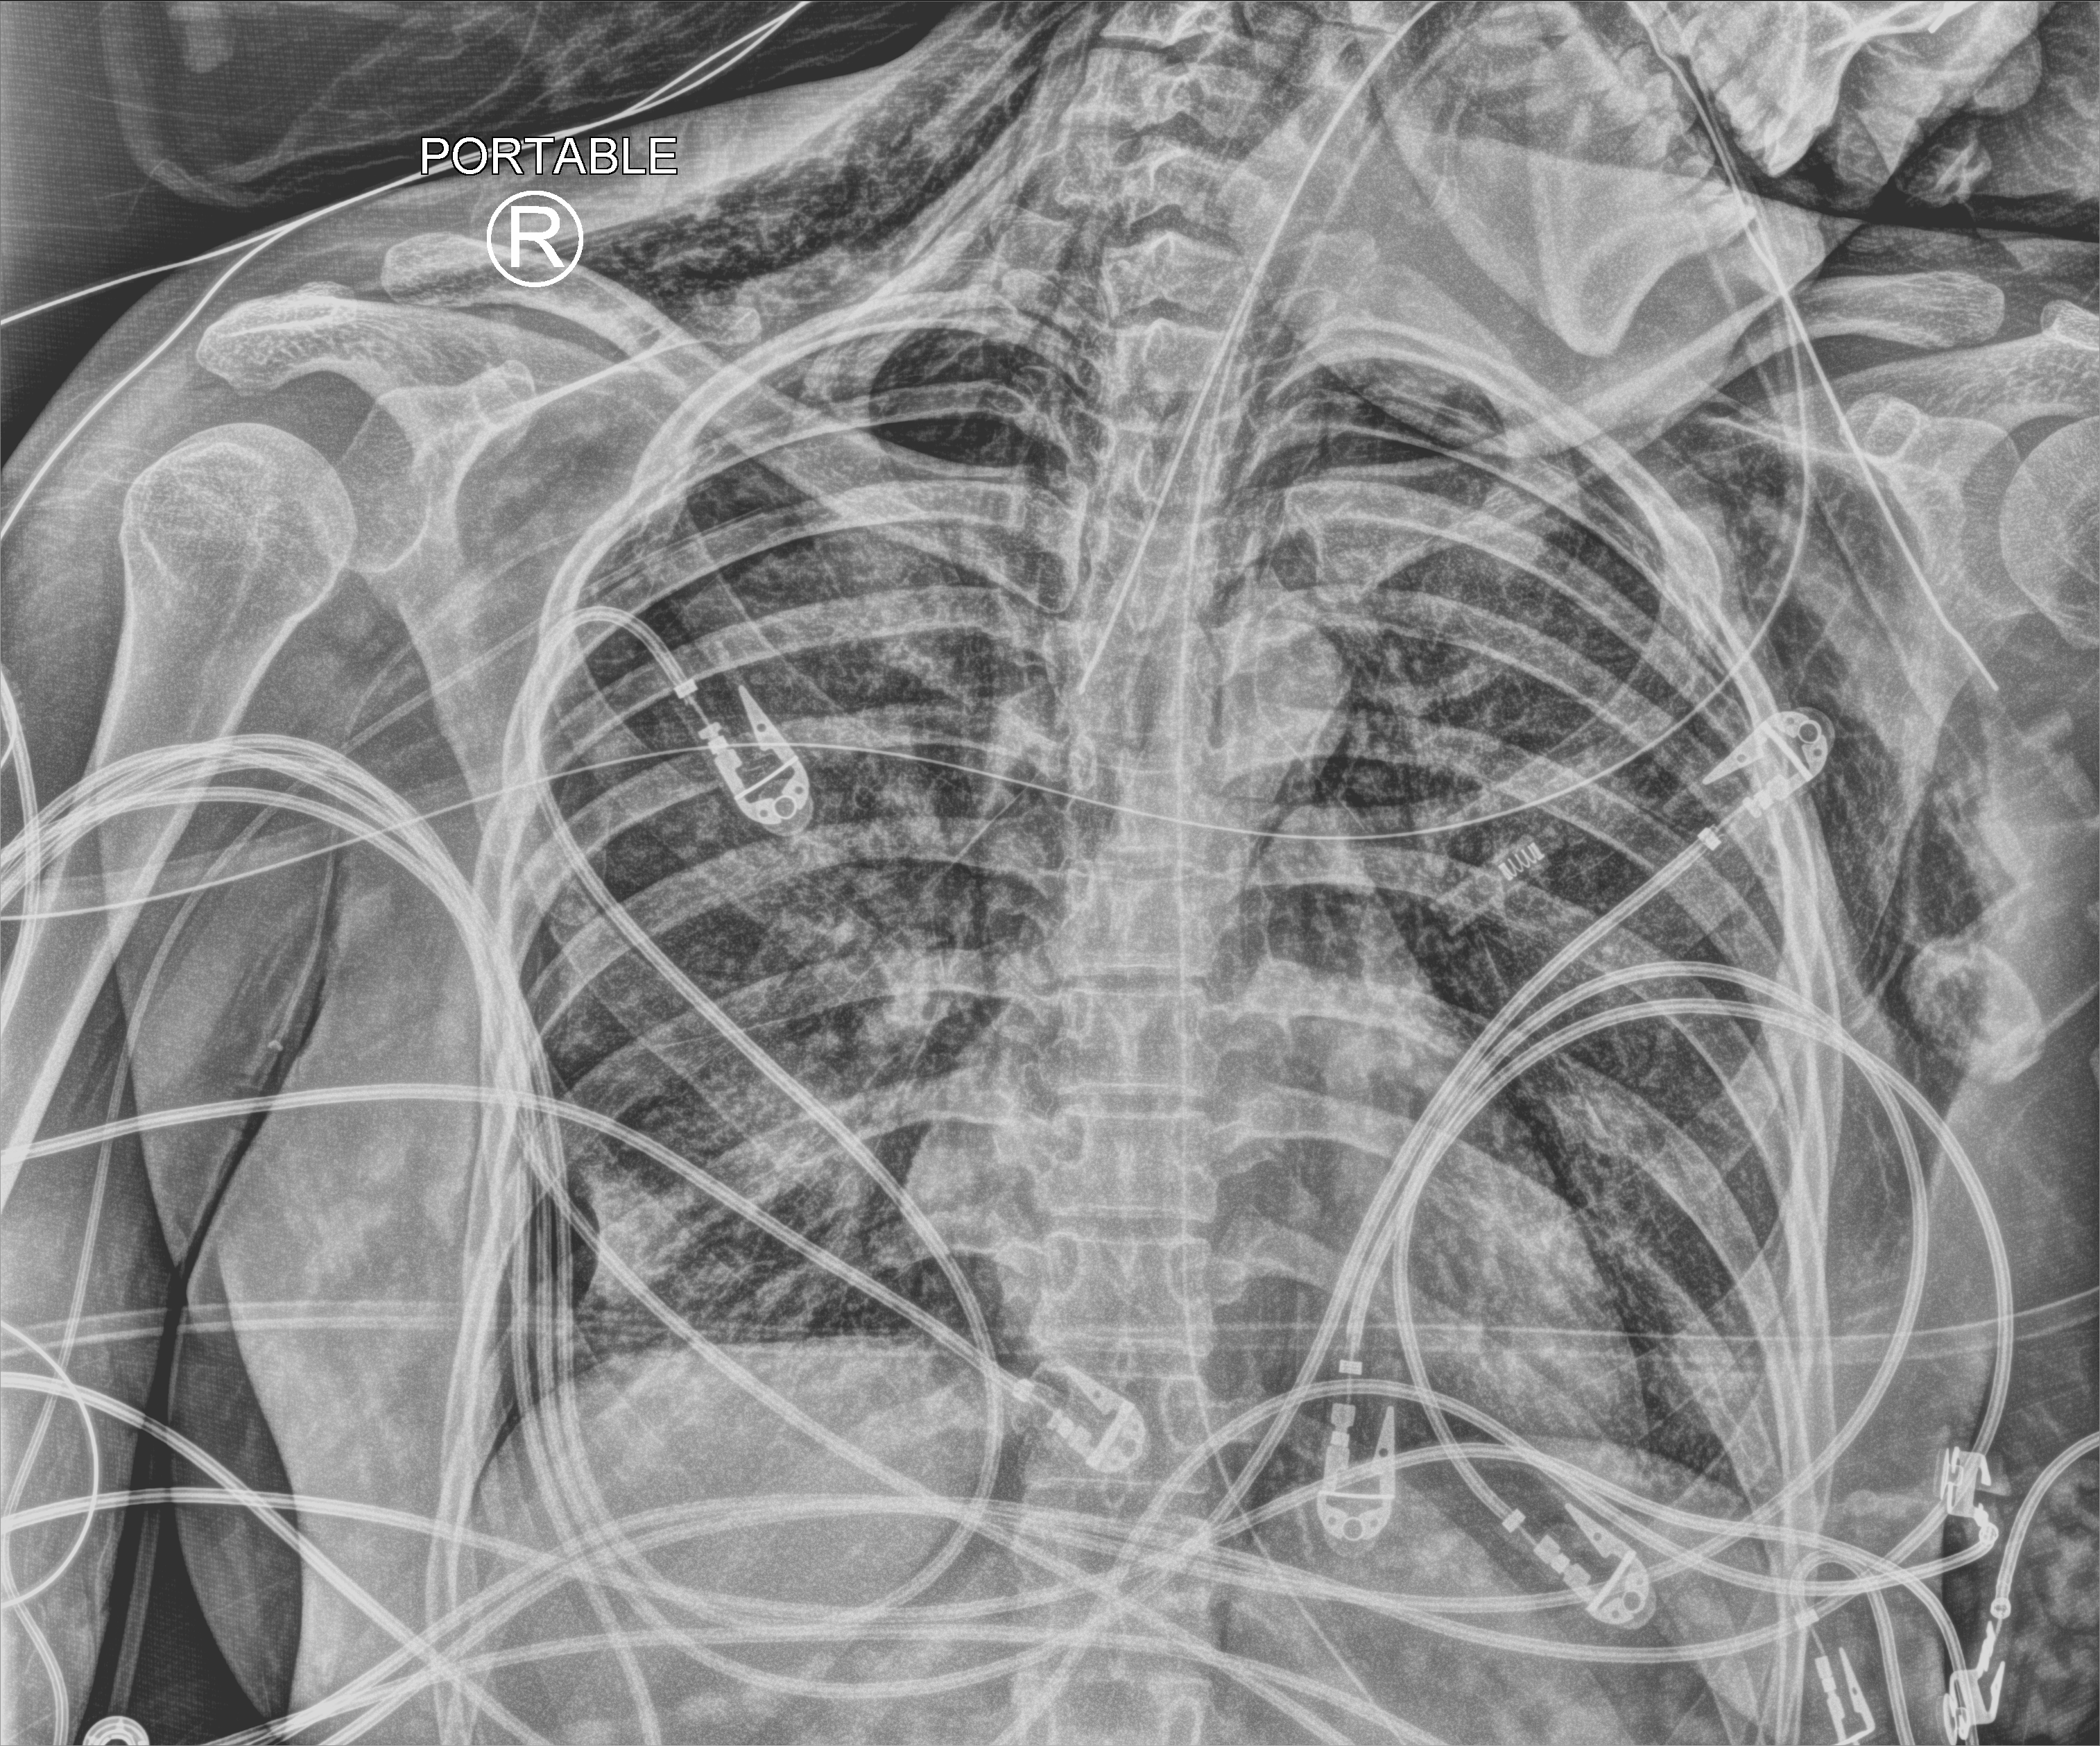
Bedside chest radiograph (computed radiography); anteroposterior (AP) projection. Patient hospitalised with COVID-19, aged 18–59 years.
Hospital-stay facts (about this admission, not read from this image; timing relative to this image not recorded): admitted to intensive care during this hospital stay: yes; COPD (admission record): no; mechanically ventilated during this hospital stay: yes.